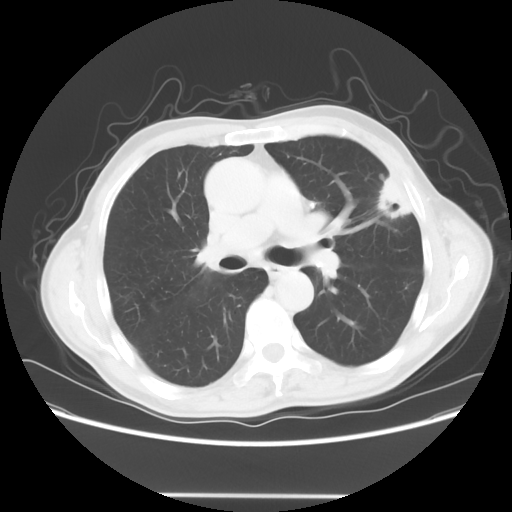
Chest CT, one axial slice; position 38 of 64 along the scan axis; 120 kVp; lung window (W 1500 / L -600 HU); 512 × 512 image matrix, field of view 392 × 392 mm. Patient: male, 71 years. Case-level facts recorded for this patient, not image findings: clinical TNM (as recorded): T1c N0 M0.
Outlined on this slice (rectangle marked by the reading radiologist):
- lung tumour (recorded histology: adenocarcinoma): bounding box [x1, y1, x2, y2] px = [375, 168, 407, 225]